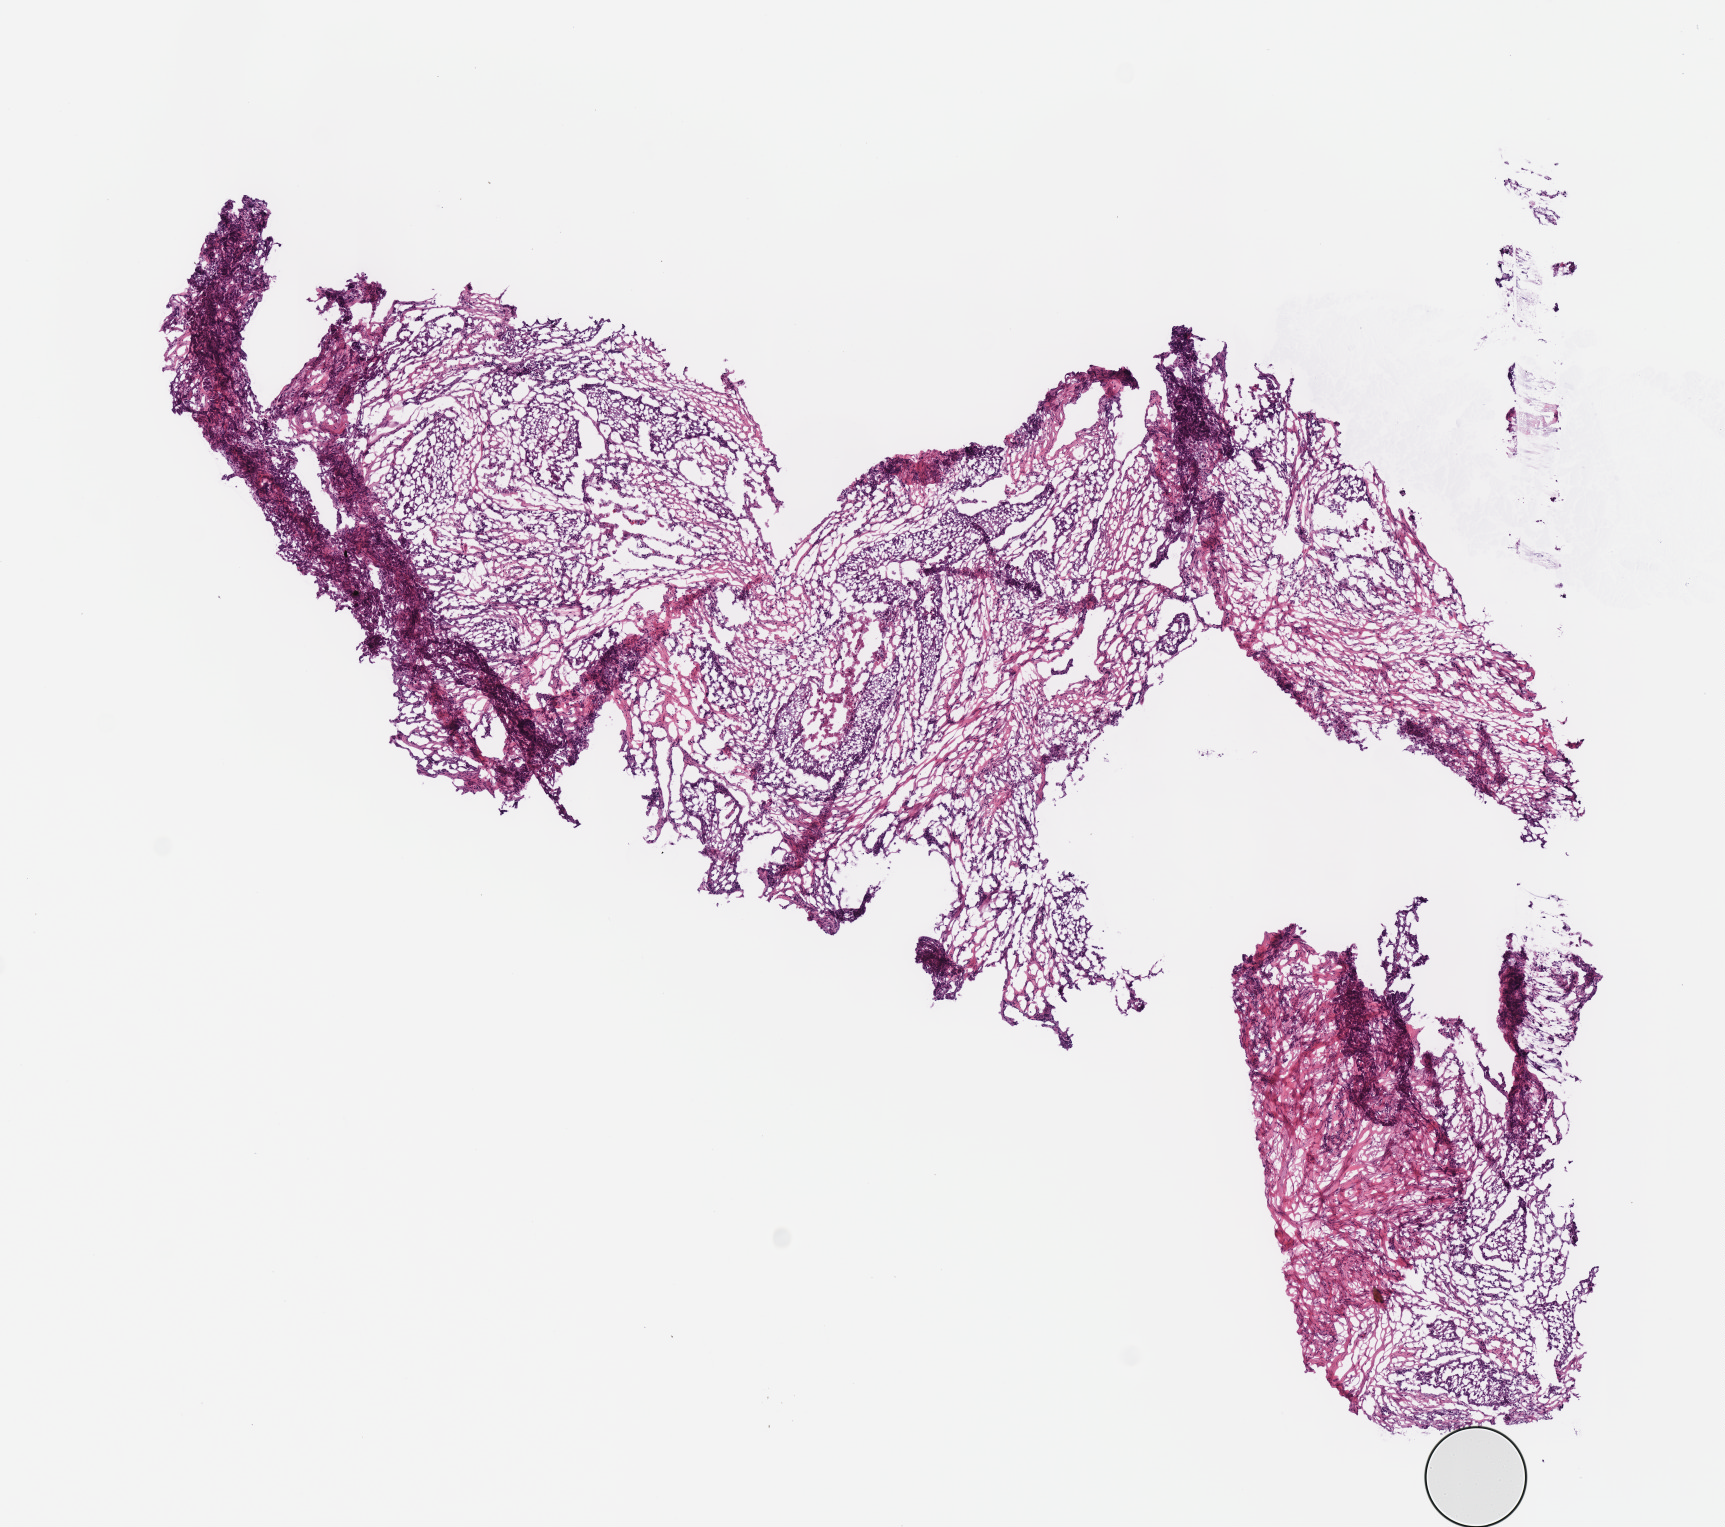
H&E whole-slide image, a low-resolution overview of the entire scanned area, about 6.8 x 6.0 mm (from a 40x scan). Frozen section from the top of the tissue portion. Sample: primary tumour, head and neck. Patient: male, age at initial diagnosis 67 years. Histologic grade: G2 (moderately differentiated). Composition of this section per pathologist review: tumour cells 75%, tumour nuclei 75%, normal cells 0%, stromal cells 25%, necrosis 0%. Inflammatory infiltration, as recorded: lymphocyte infiltration 10%, monocyte infiltration 0%, neutrophil infiltration 0%.
Diagnosis: Squamous cell carcinoma, NOS (larynx, NOS). AJCC pathologic stage: IVA (7th edition).